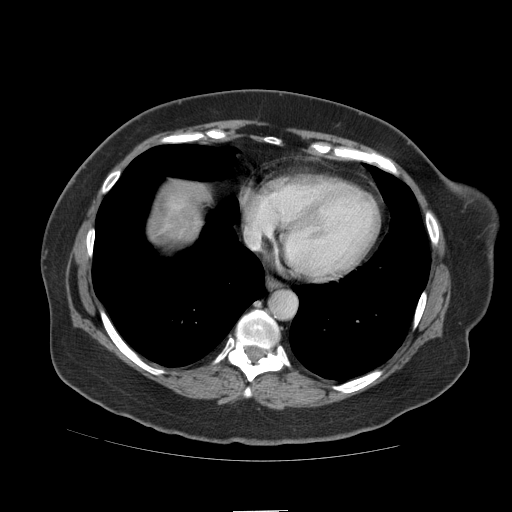
Contrast-enhanced abdominal CT (liver protocol), one axial slice. Position 102 of 109 along the scan axis. 140 kVp. Soft-tissue window (W 400 / L 40 HU). 2.5 mm slice thickness. 512 × 512 image matrix. From the clinical record (not read from this slice): diagnosis: hepatocellular carcinoma (patient treated with transarterial chemoembolisation; whether this scan precedes or follows treatment is not stated here); TNM stage (as recorded): Stage-IVB; Child-Pugh class: A; tumour differentiation: poorly differentiated.
Structures marked on this image (semi-automatically segmented with operator editing):
- liver parenchyma outside the tumour (the mass and vessels are separate outlines, so this box may not span the whole liver): bounding box <150,178,208,242> (left, top, right, bottom; pixels)